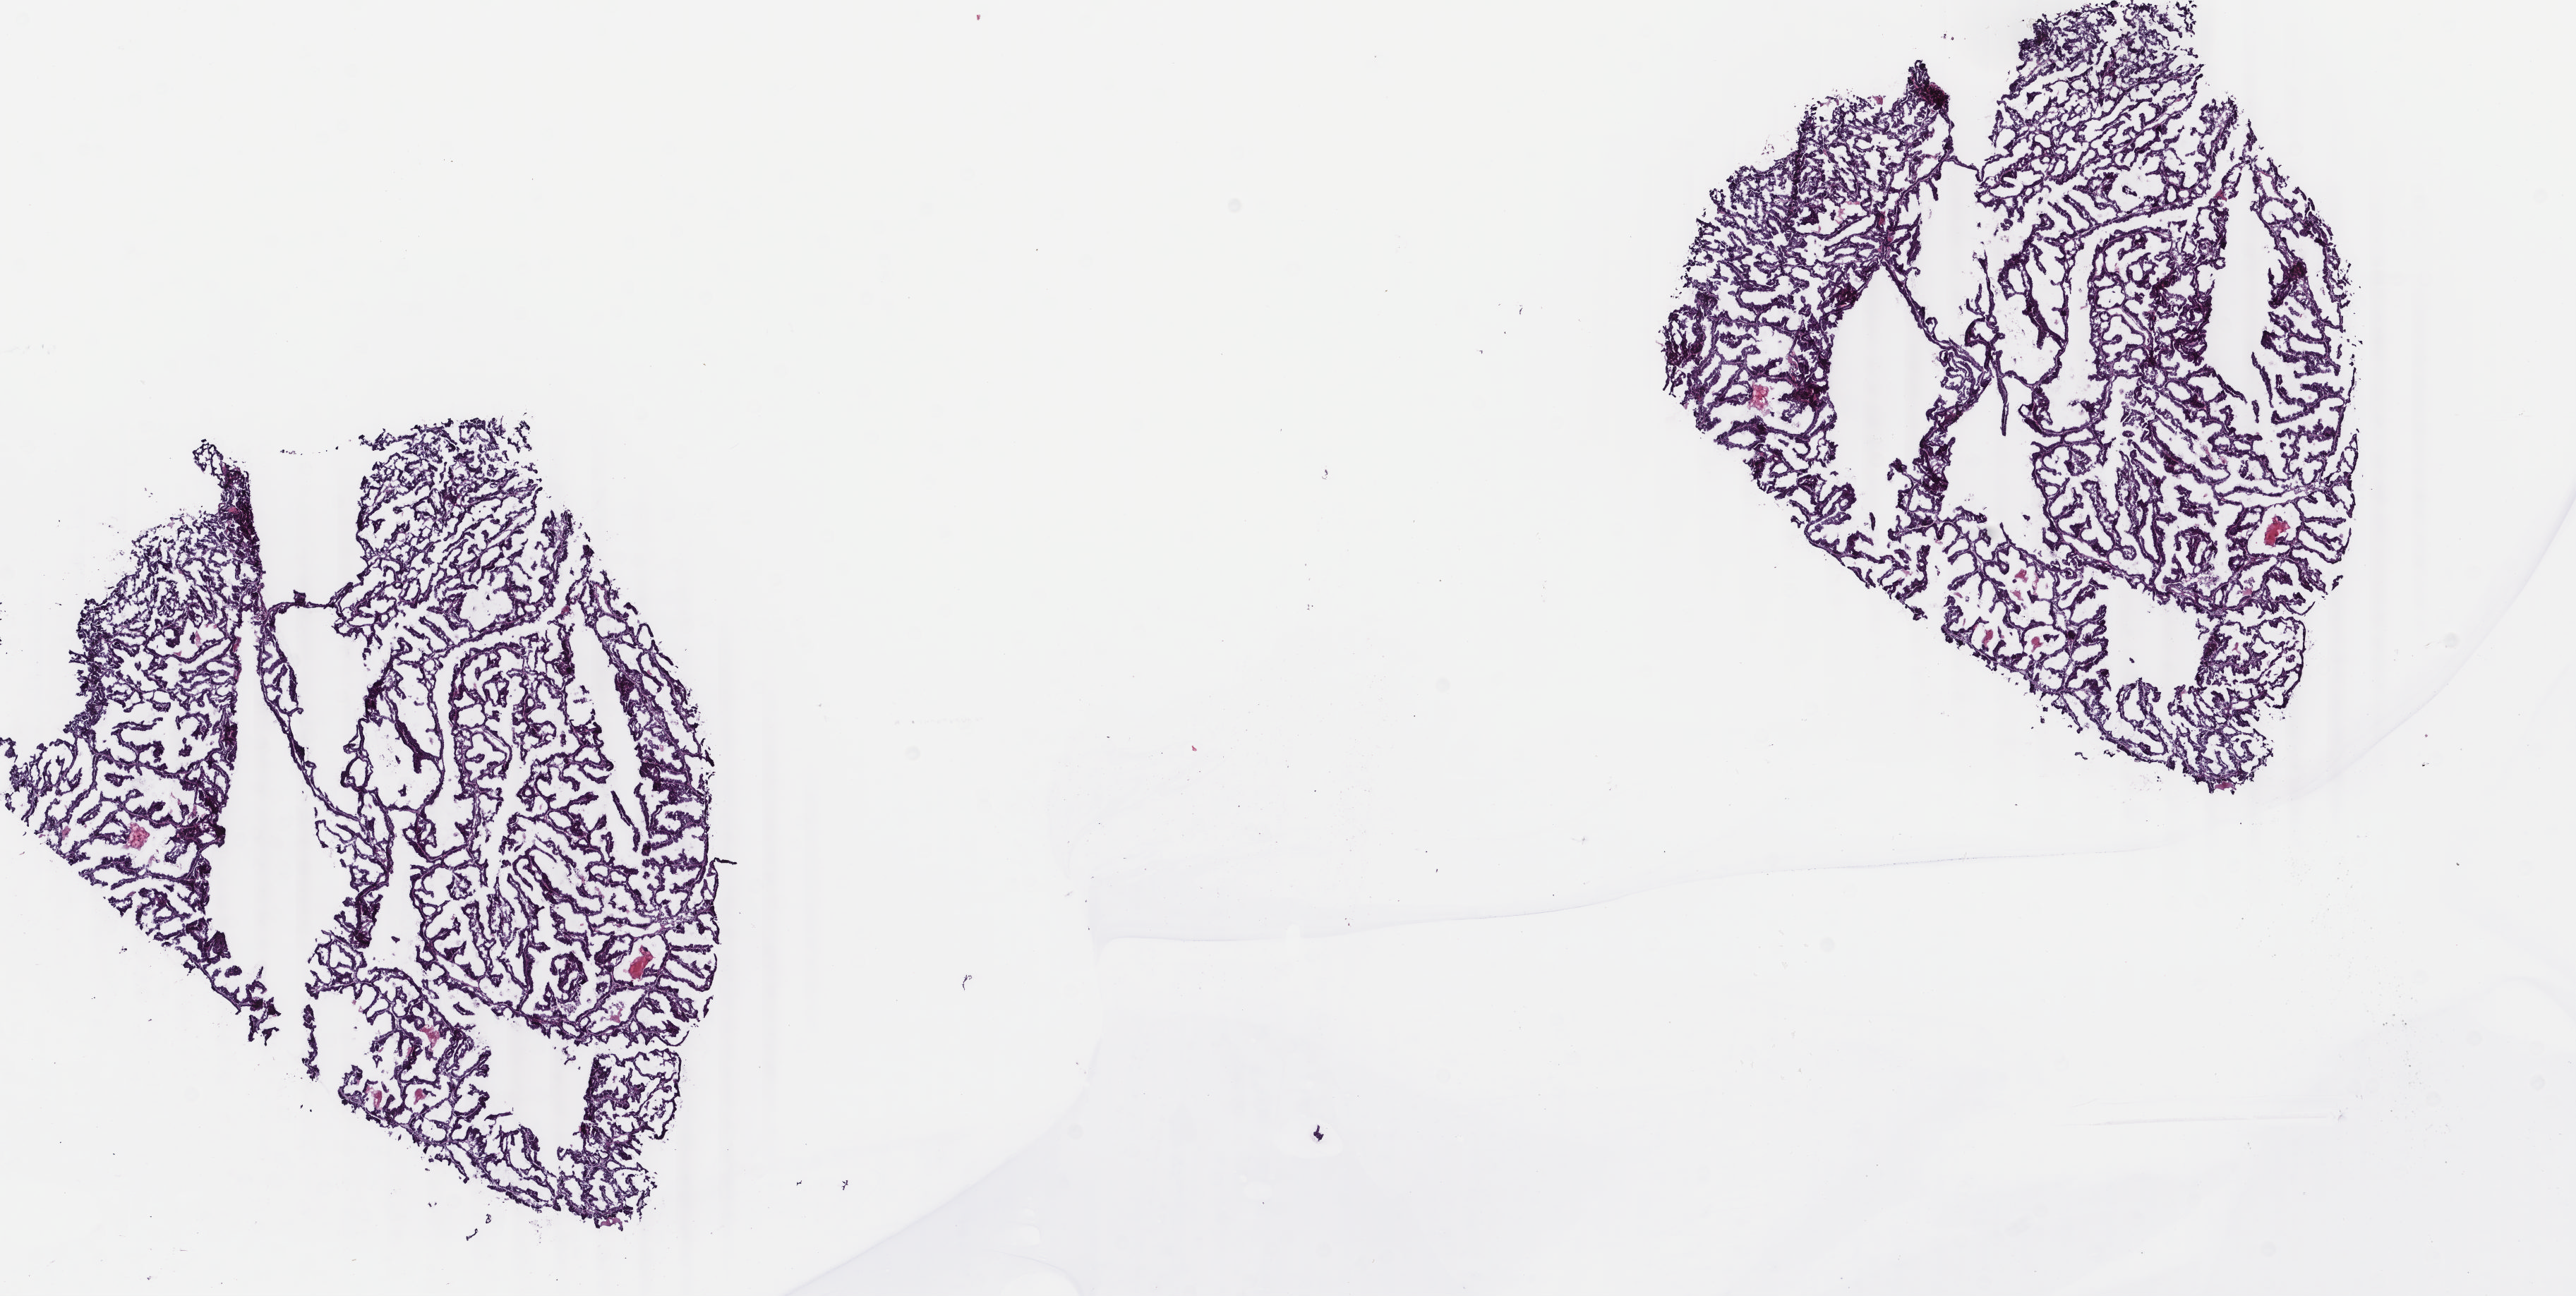
Whole-slide histology image, H&E-stained — a low-resolution overview of the entire scanned area, about 14.5 x 7.3 mm (from a 40x scan); frozen section from the bottom of the tissue portion; sample: primary tumour, uterus. Female, age 71 years at initial diagnosis. Histologic grade: G1 (well differentiated). Slide review estimates, as recorded: tumour cells 95%, tumour nuclei 95%, normal cells 0%, stromal cells 5%, necrosis 0%. Infiltration values recorded for this section: lymphocyte infiltration 4%, monocyte infiltration 4%, neutrophil infiltration 0%.
* FIGO stage: IA
* histologic diagnosis: Endometrioid adenocarcinoma, NOS (endometrium)